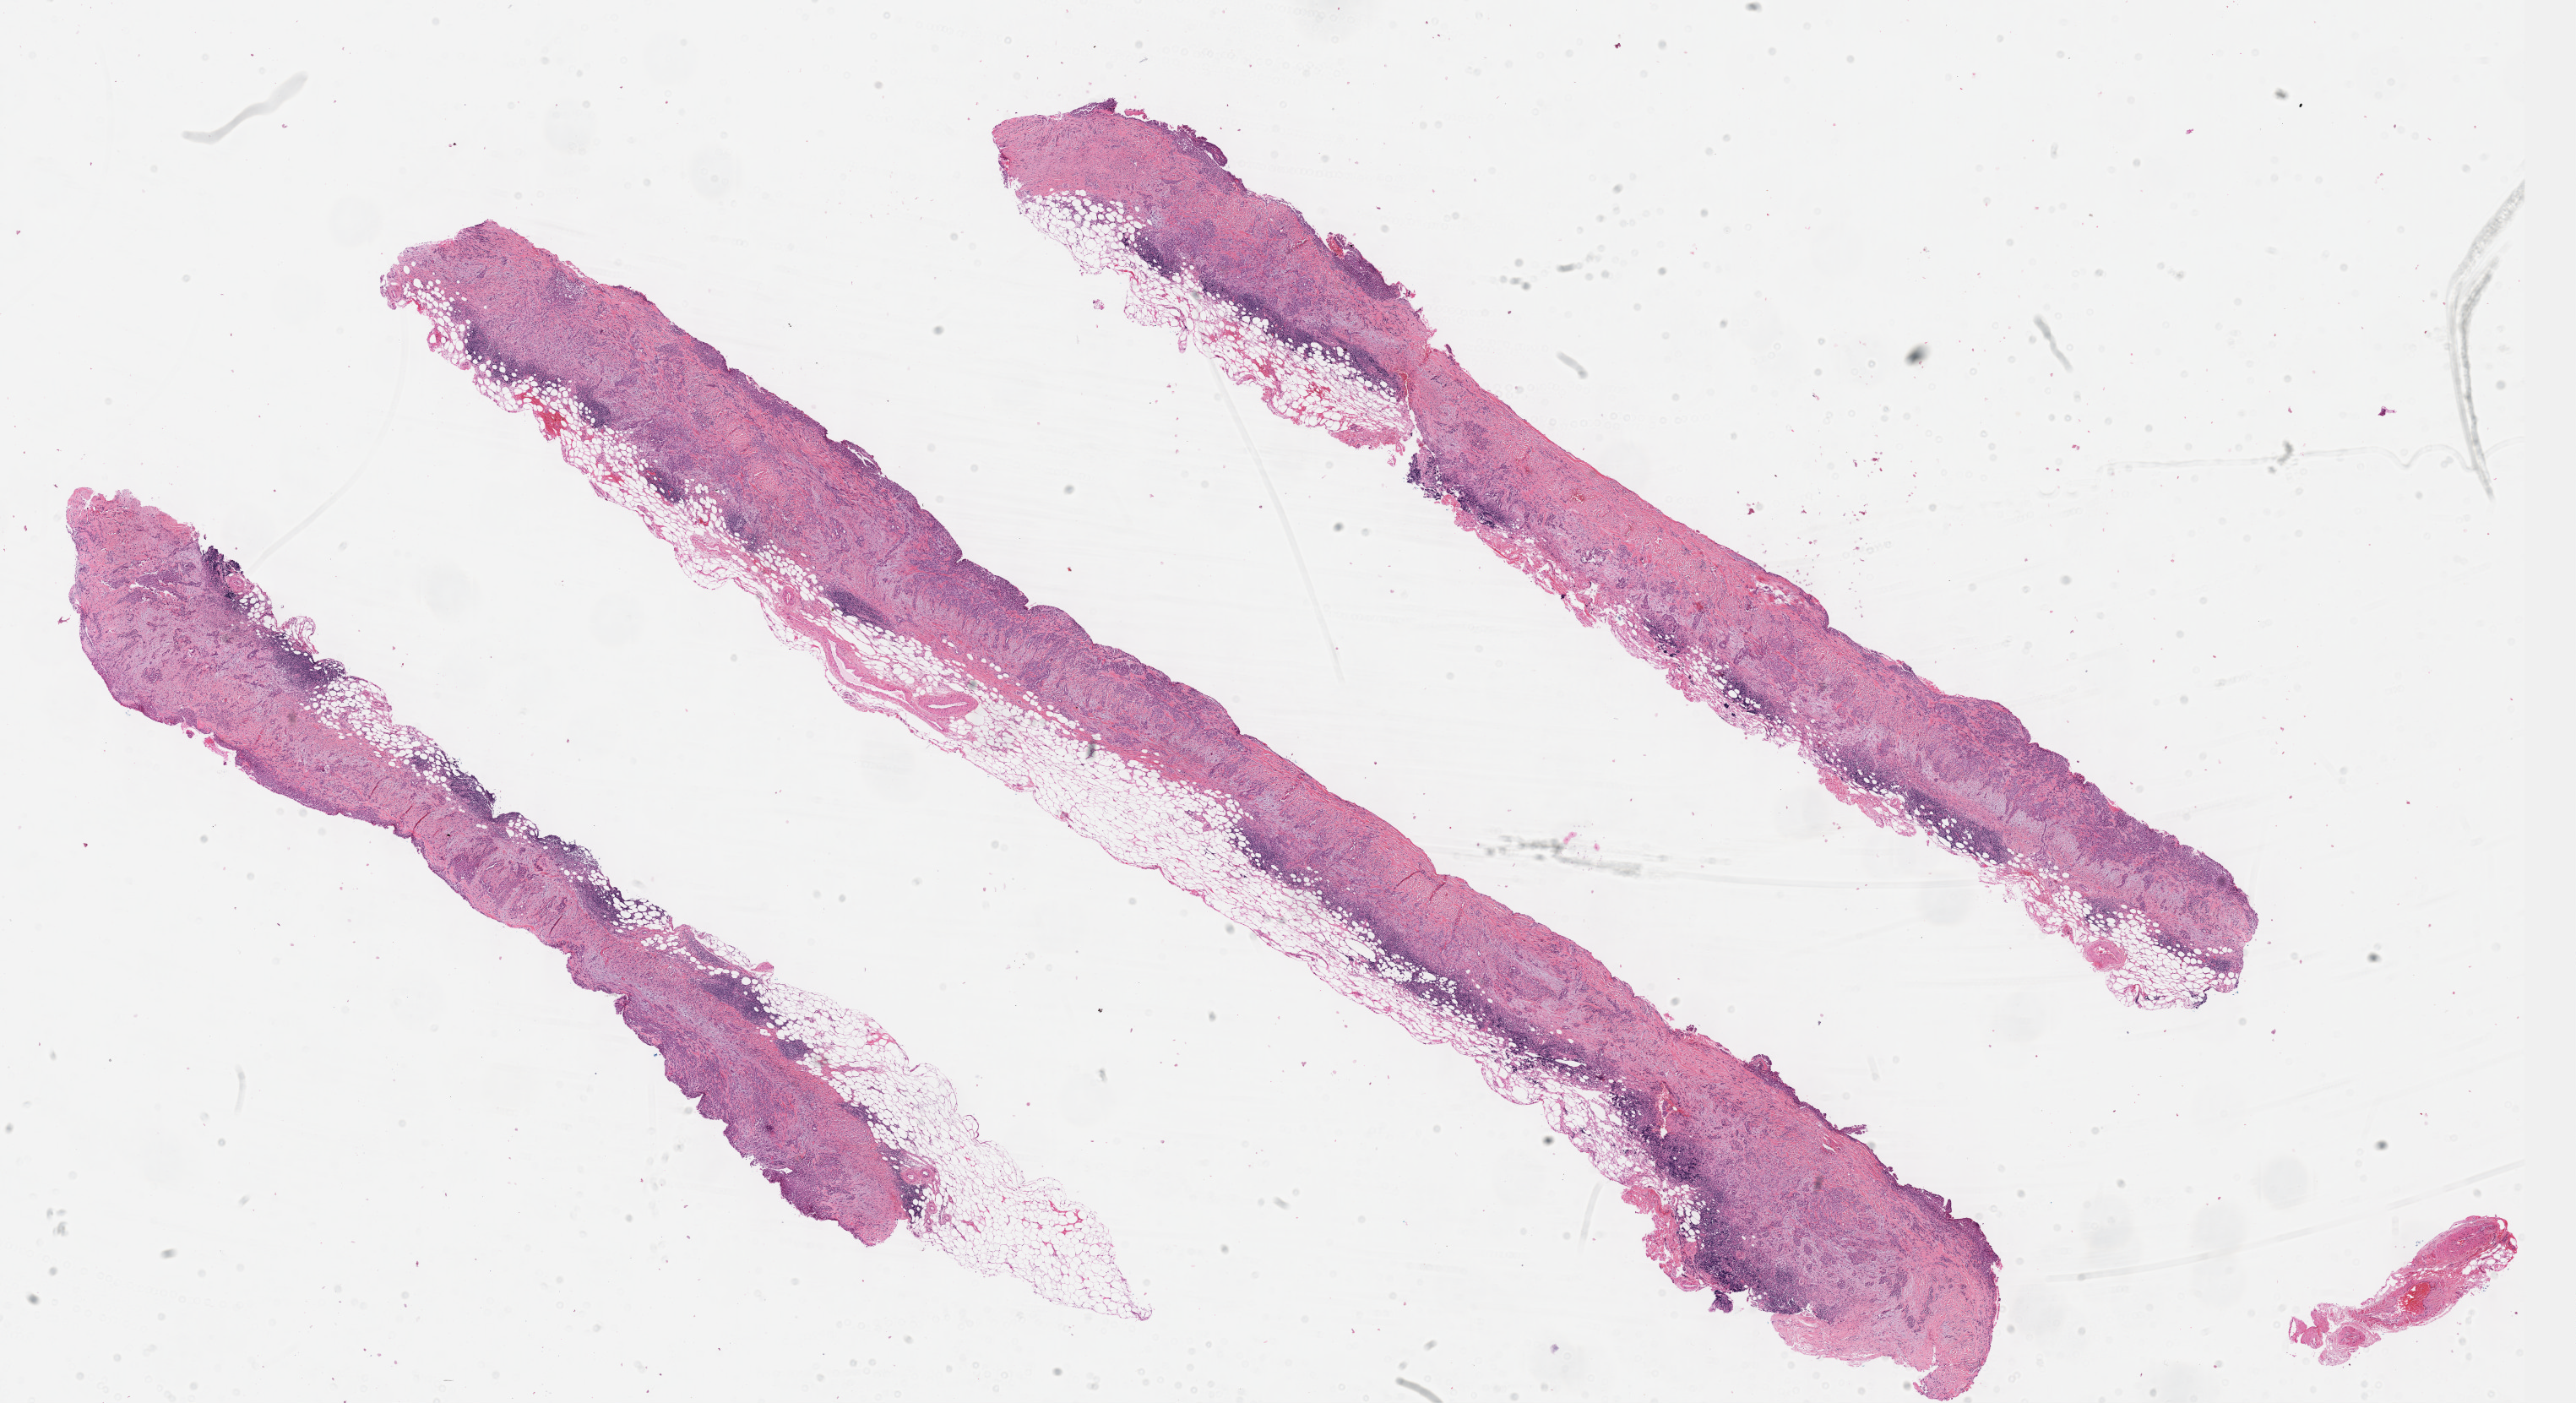
H&E-stained whole-slide image — shown as a low-resolution overview of the whole scanned area (about 24.6 x 13.4 mm, from a 40x scan). Formalin-fixed paraffin-embedded (FFPE) diagnostic section. Sample: primary tumour, mesothelium. Male, age 66 years at initial diagnosis.
TNM: T2 N0 M0. Pathologic diagnosis: Epithelioid mesothelioma, malignant (pleura, NOS). Laterality: left. AJCC pathologic stage: II.